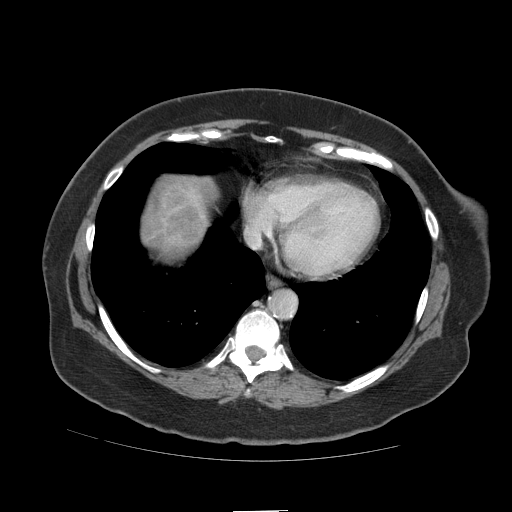
Contrast-enhanced abdominal CT (liver protocol), one axial slice. Reconstruction kernel STANDARD. Soft-tissue window (W 400 / L 40 HU). 2.5 mm slice thickness. 512 × 512 image matrix, field of view 420 × 420 mm. Case-level facts recorded for this patient, not image findings: diagnosis: hepatocellular carcinoma (patient treated with transarterial chemoembolisation; whether this scan precedes or follows treatment is not stated here); TNM stage (as recorded): Stage-IVB; Child-Pugh class: A; tumour differentiation: poorly differentiated; tumour nodularity: multinodular.
Annotated regions visible in this slice (semi-automatically segmented with operator editing):
- liver parenchyma outside the tumour (the mass and vessels are separate outlines, so this box may not span the whole liver): box from (x=142, y=174) to (x=212, y=254) px